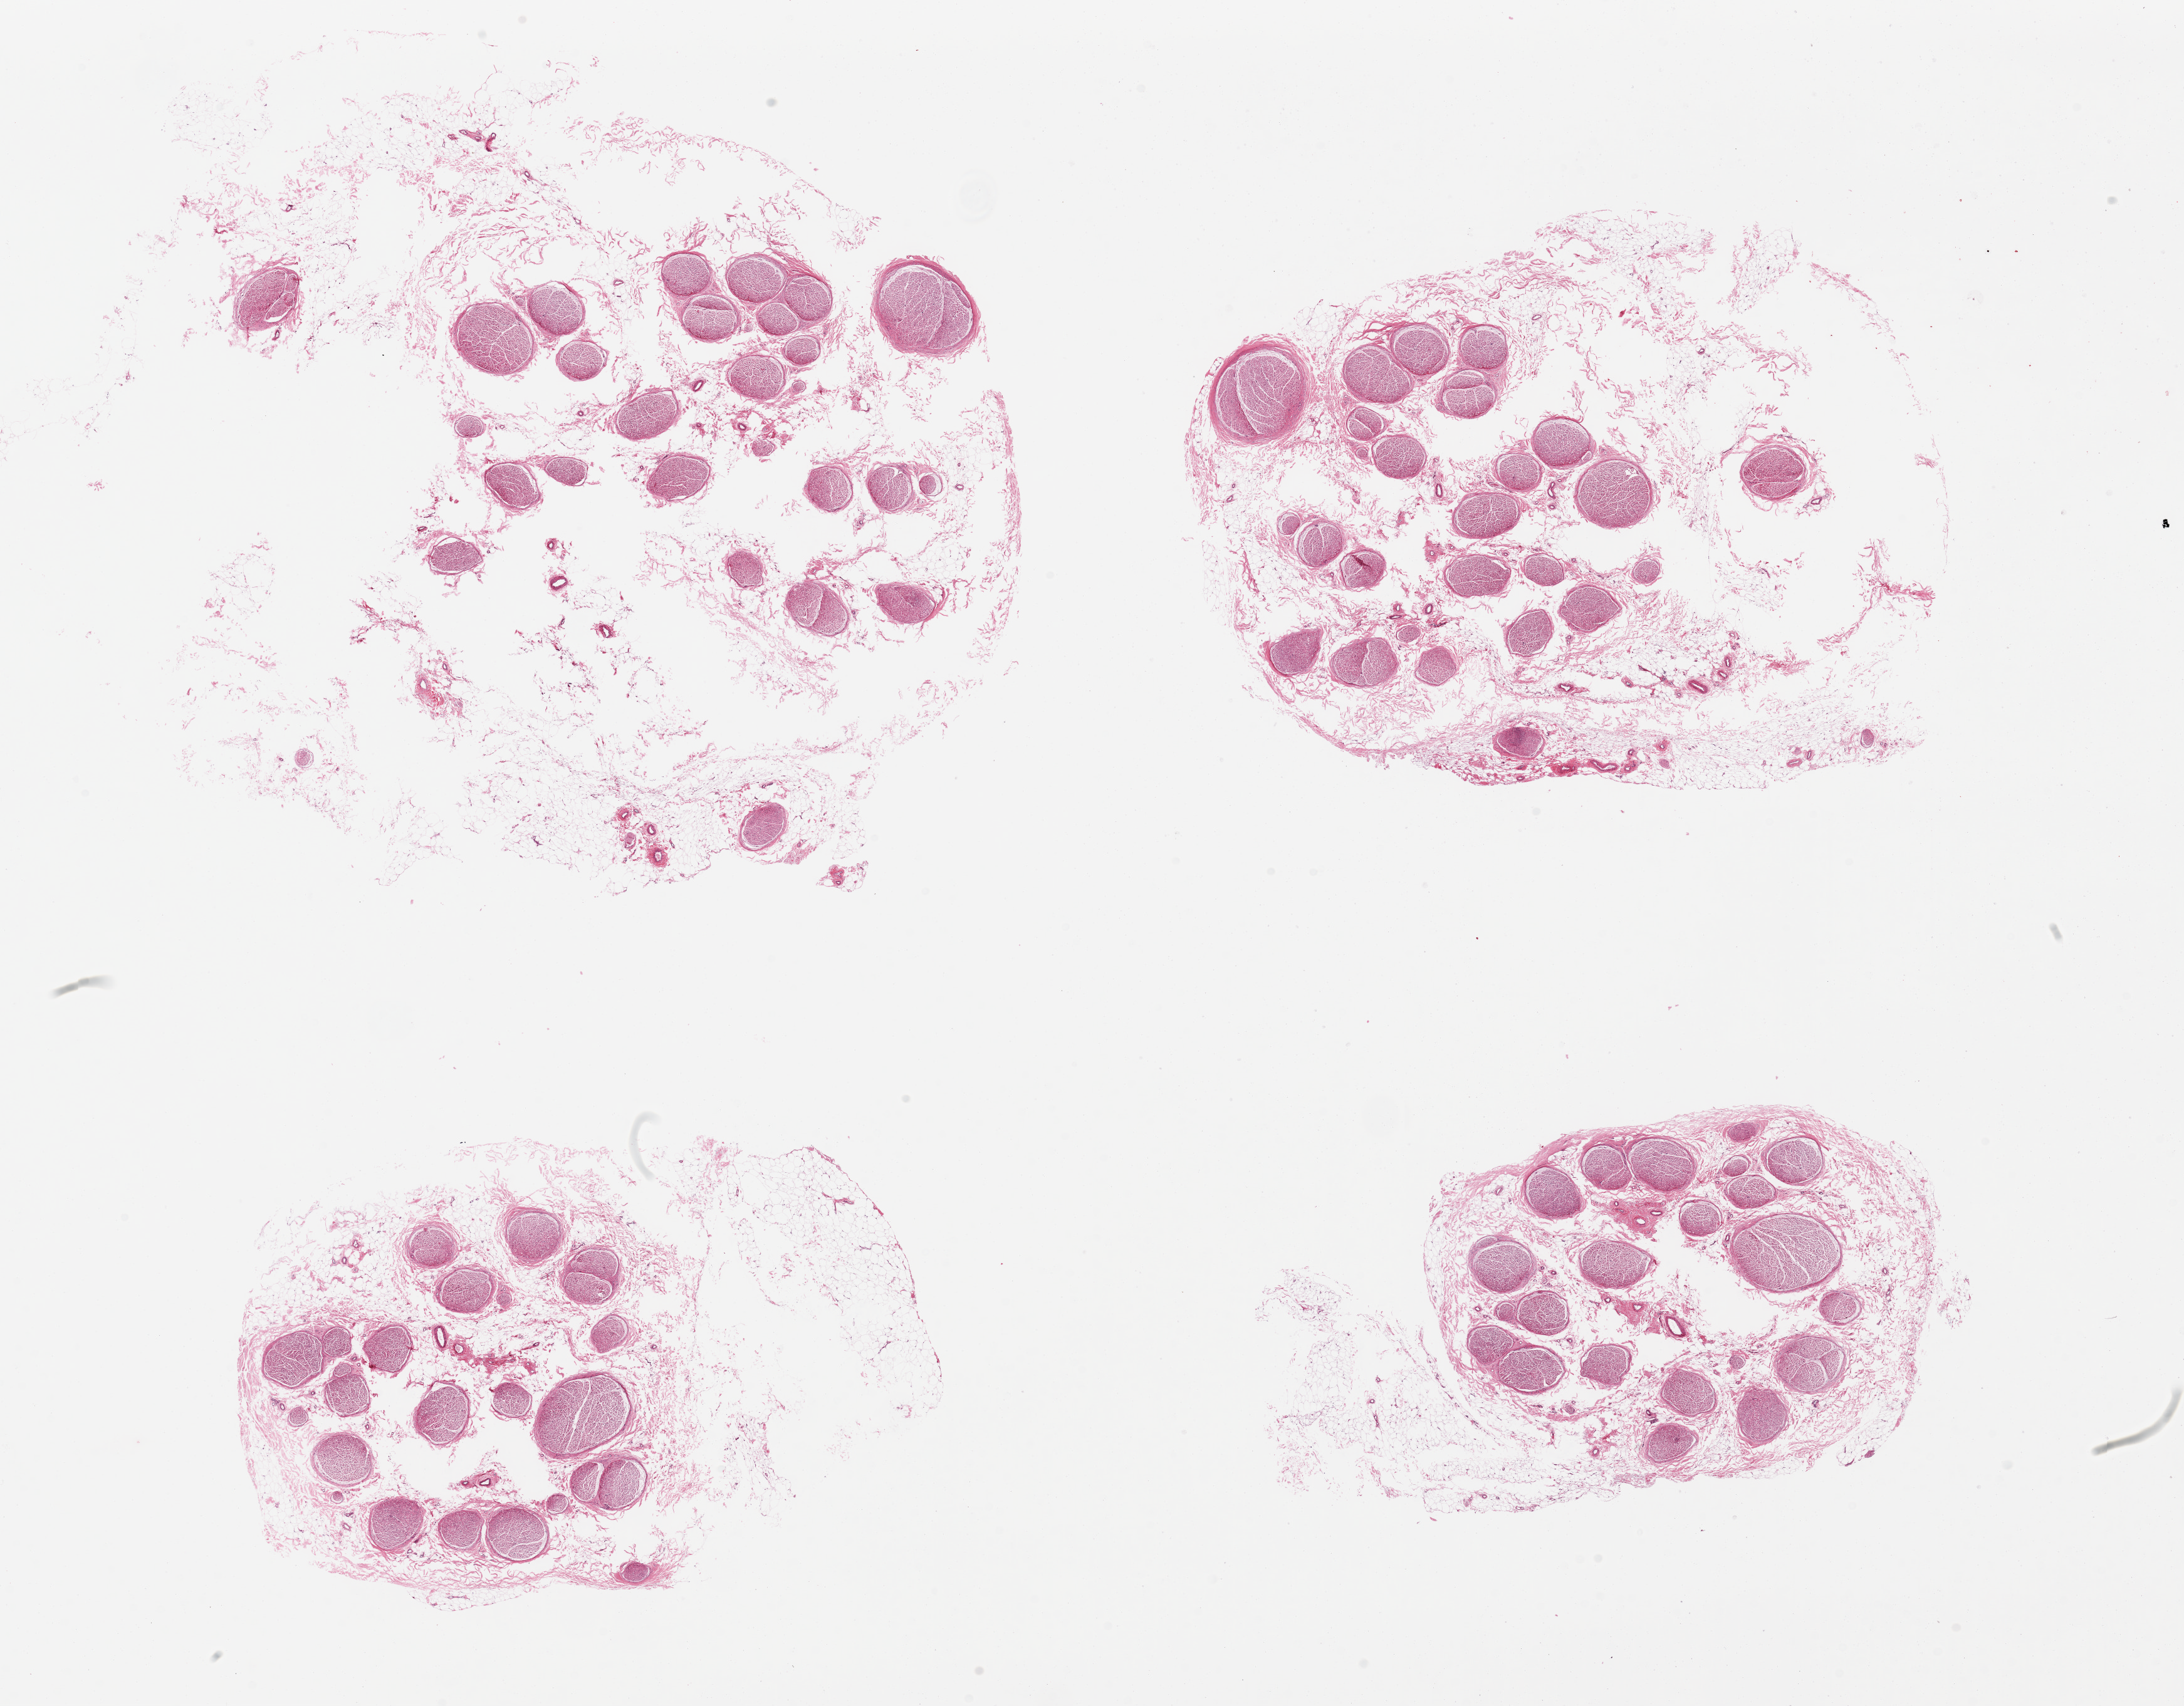
Digitized haematoxylin and eosin-stained section — whole scanned area (about 27.6 x 21.5 mm) shown as a low-resolution overview, PAXgene-fixed, paraffin-embedded tissue, section of tibial nerve (target tissue), donor tissue sample.
Review note (as recorded): 4 pieces, sections not intact, but all appear to have up to ~50% fat (attached and internal).